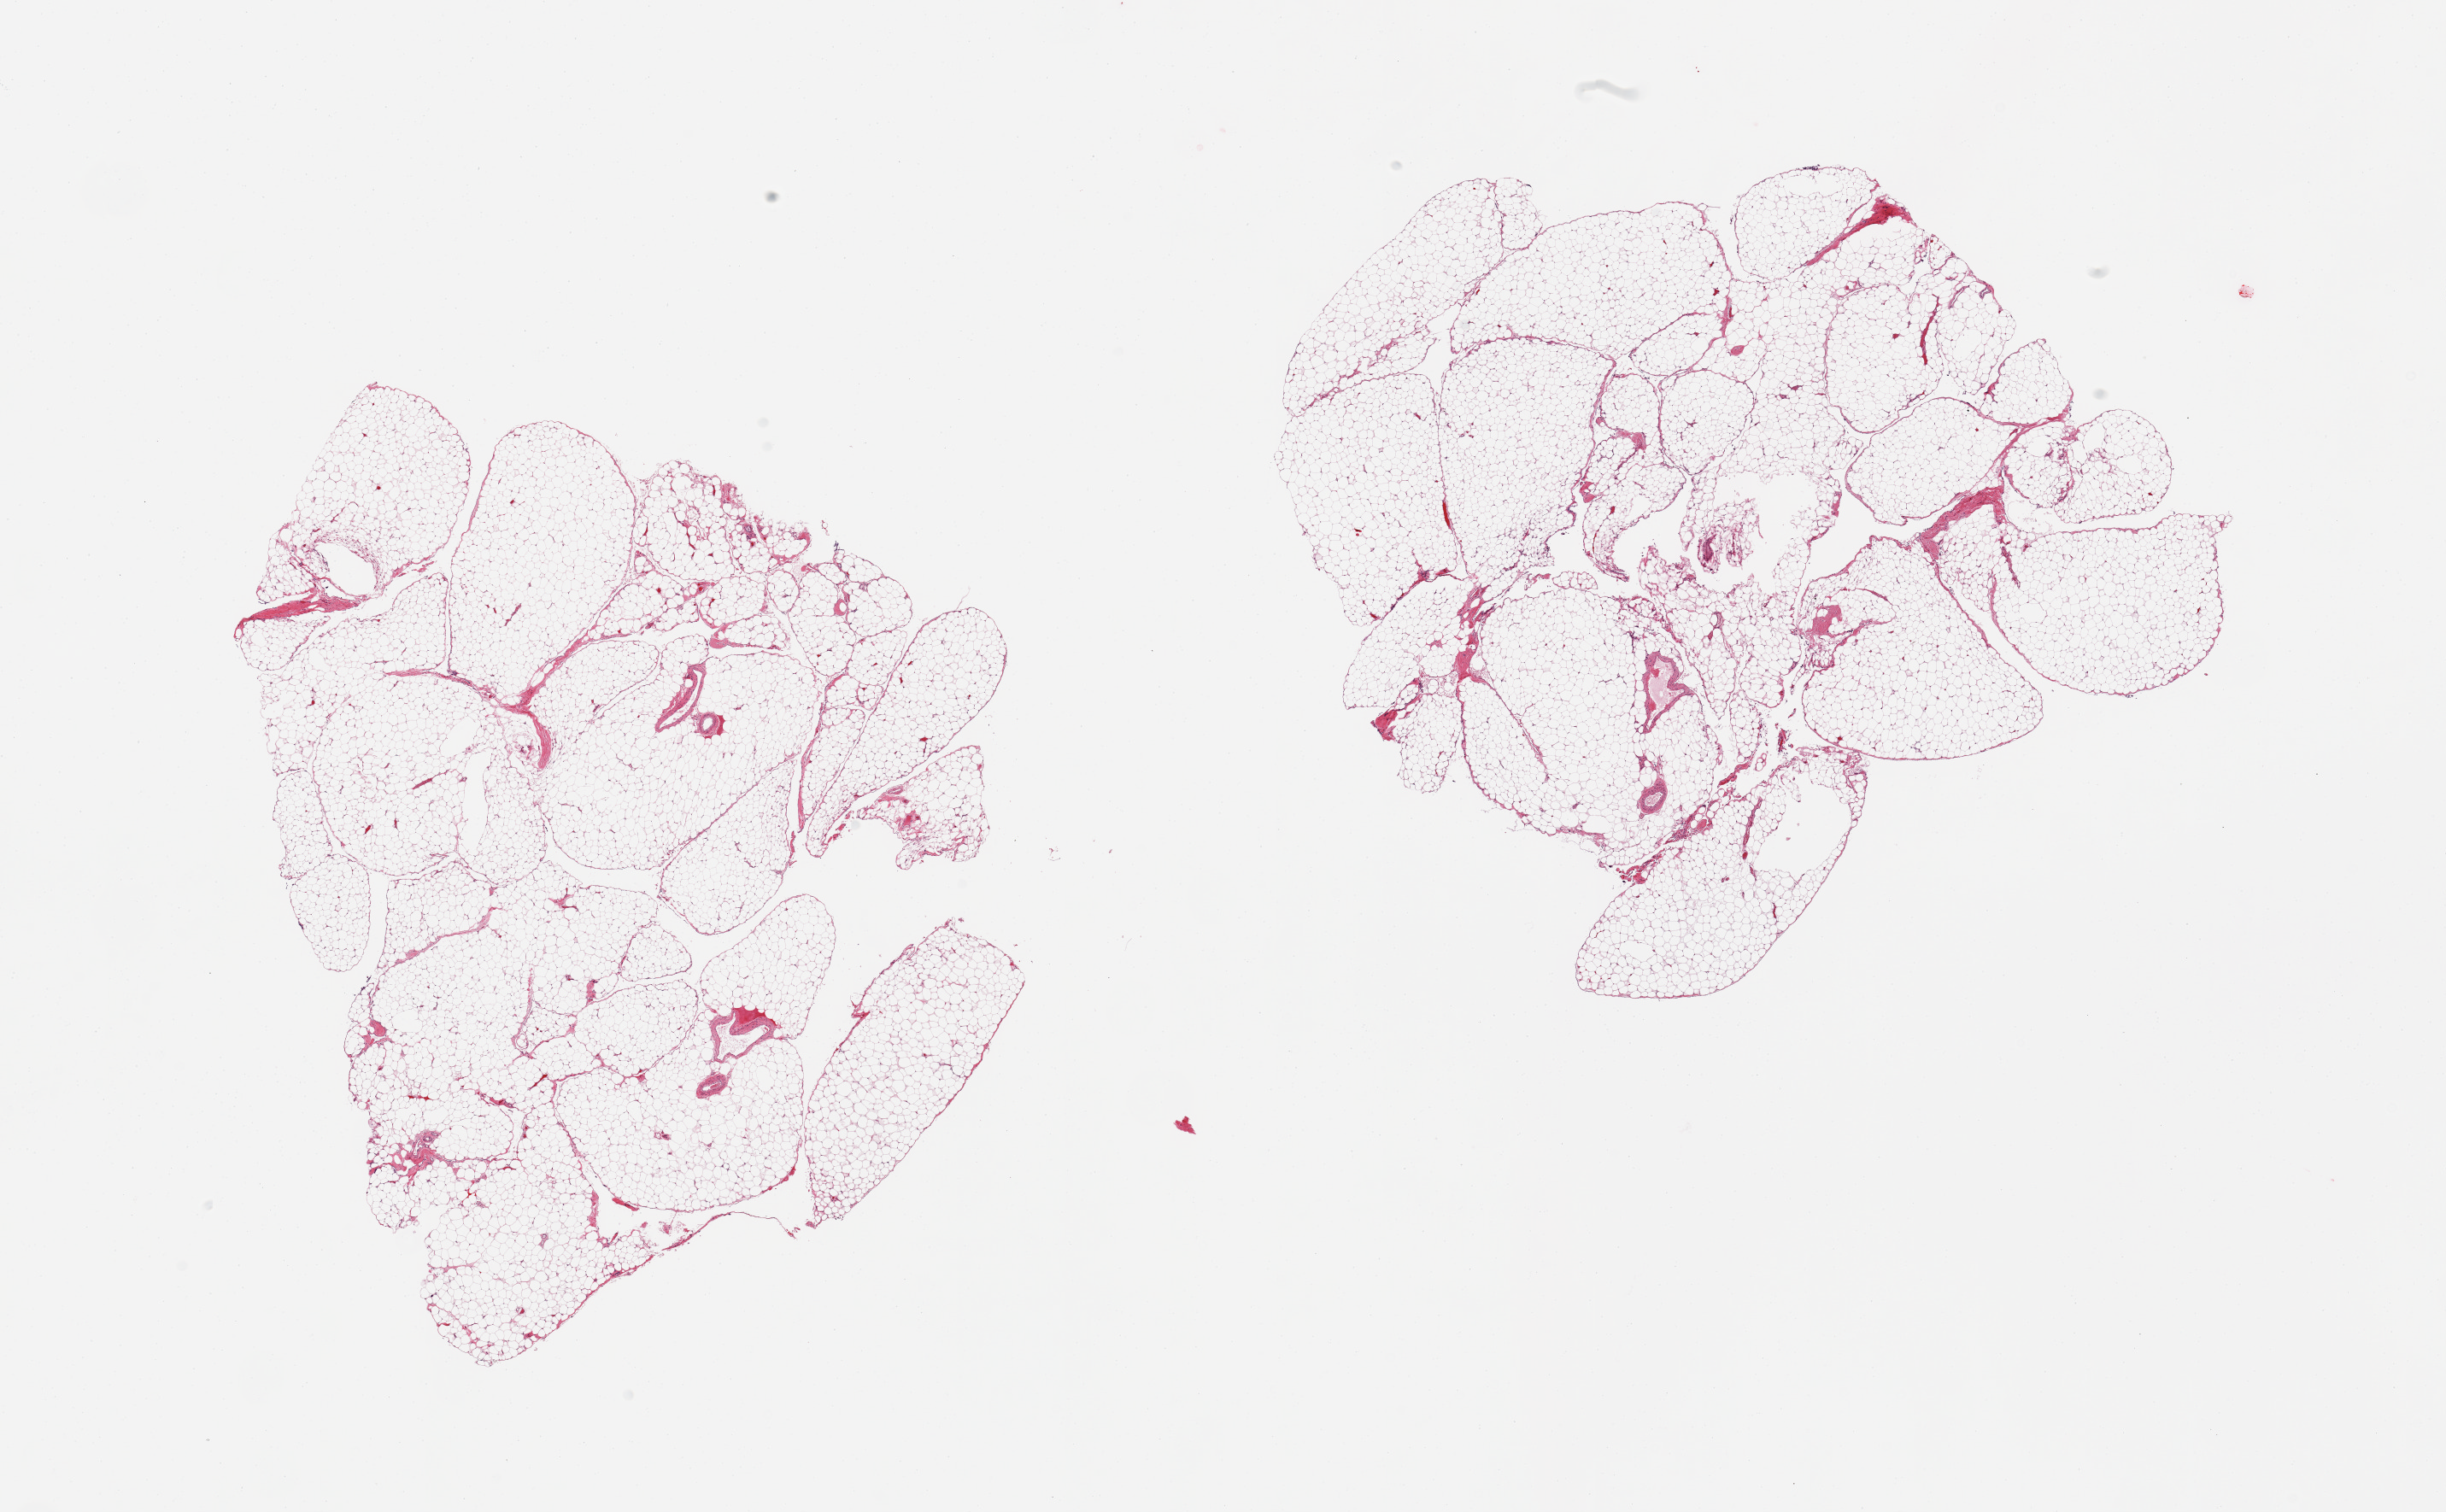
Digitized haematoxylin and eosin-stained section, brightfield, shown as a low-resolution overview of the whole scanned area (about 22.6 x 14.0 mm, acquisition: 20x scan); PAXgene-fixed paraffin-embedded (PFPE) section; section of omentum (target tissue); donor tissue sample. Male donor.
- reviewer comment on this tissue sample: 2 pieces, minimal fascia/vascular elements